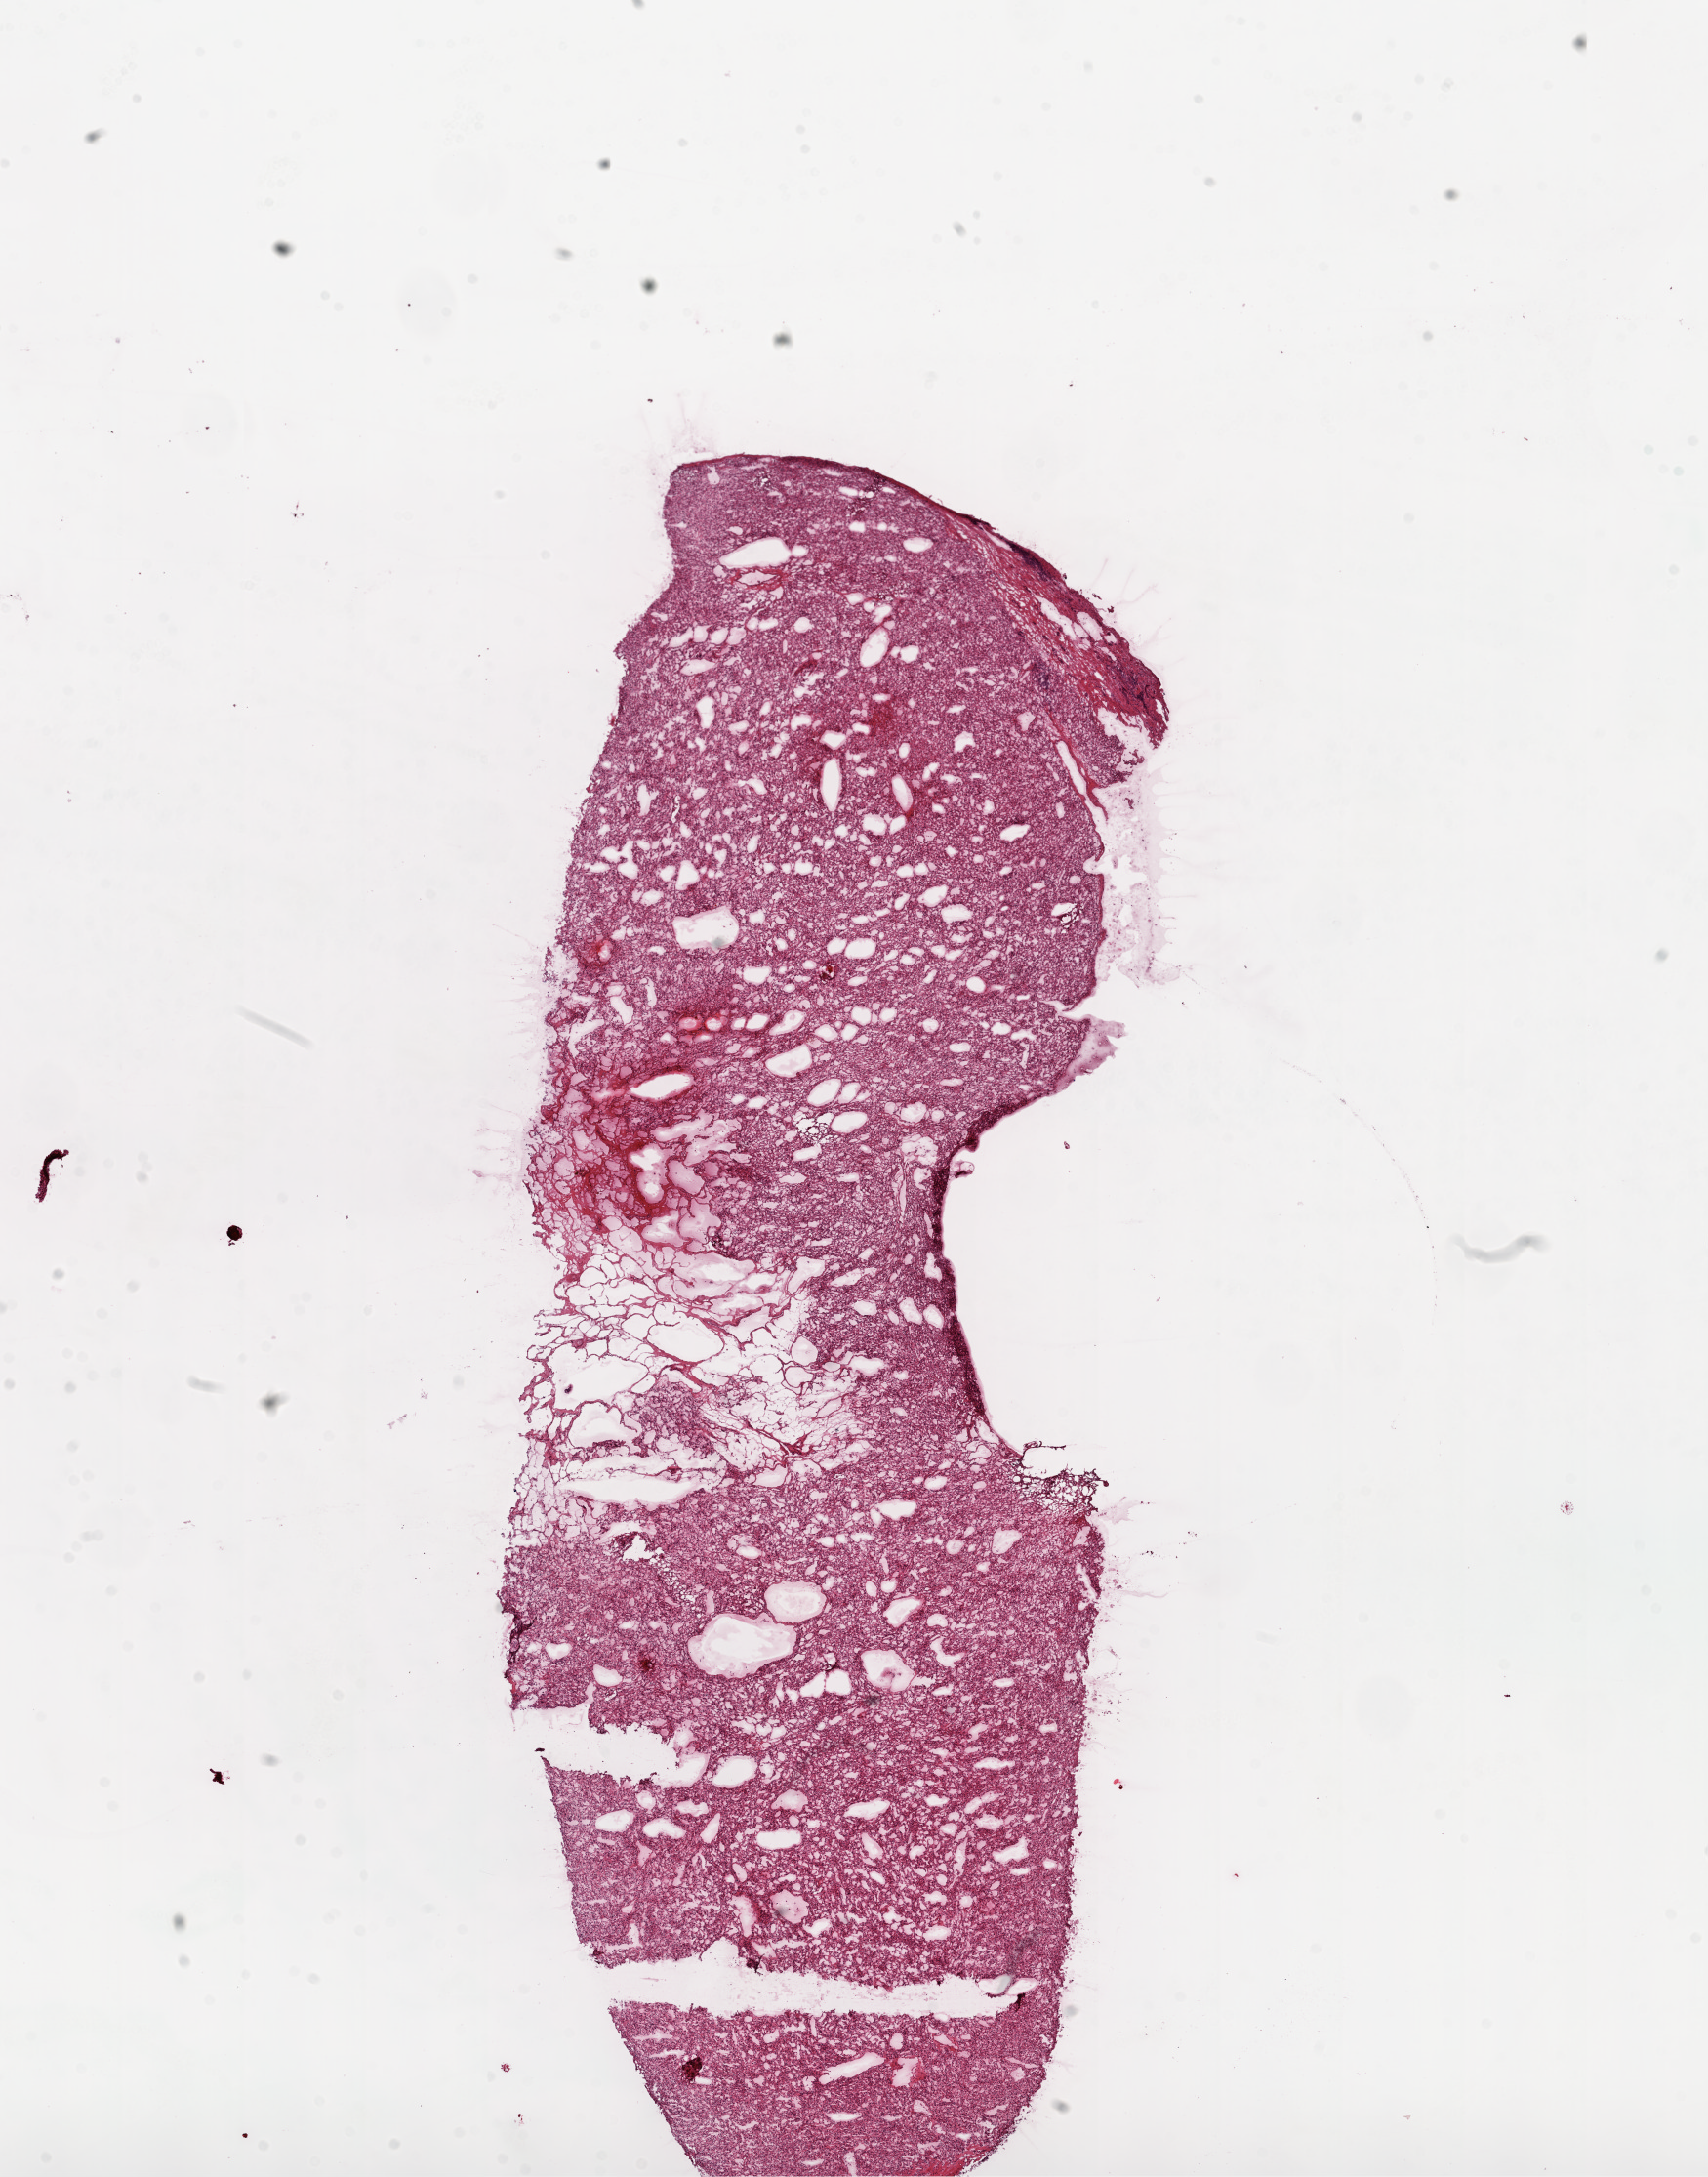
Hematoxylin and eosin (H&E) stained whole-slide image — whole scanned area (about 14.0 x 17.9 mm, from a 20x scan) shown as a low-resolution overview; frozen section; primary tumour sample from the kidney. Patient: male, age at initial diagnosis 52 years. Histologic grade: G2 (moderately differentiated). Composition of this section per pathologist review: tumour cells 98%, tumour nuclei 95%, stromal cells 2%, necrosis 0%. Infiltration values recorded for this section: lymphocyte infiltration 2%.
* TNM: T1a NX M0
* AJCC pathologic stage: I
* diagnosis: Clear cell adenocarcinoma, NOS